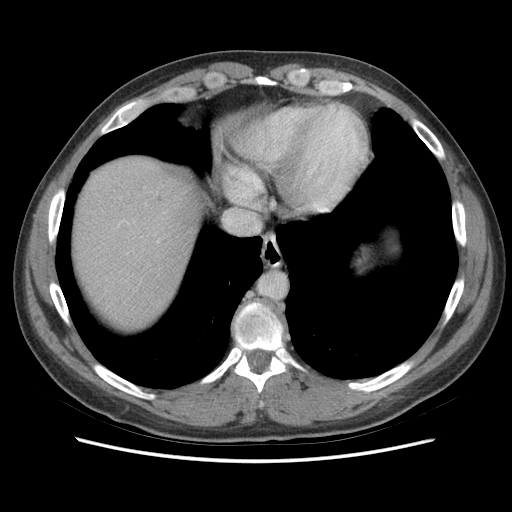
Contrast-enhanced abdominal CT (liver protocol), one axial slice. Slice 65 of 73 in the series (ordered by position). Reconstruction kernel STANDARD. Soft-tissue window (W 400 / L 40 HU). 2.5 mm slice thickness. 512 × 512 image matrix, field of view 360 × 360 mm. From the clinical record (not read from this slice): diagnosis: hepatocellular carcinoma (patient treated with transarterial chemoembolisation; whether this scan precedes or follows treatment is not stated here); TNM stage (as recorded): Stage-IIIA; Child-Pugh class: A; tumour nodularity: multinodular.
Outlined on this slice (semi-automatic segmentation, software-assisted and operator-edited):
- abdominal aorta: bounding box <260,274,287,299> (left, top, right, bottom; pixels)
- liver parenchyma outside the tumour (the mass and vessels are separate outlines, so this box may not span the whole liver): <72,156,198,324>